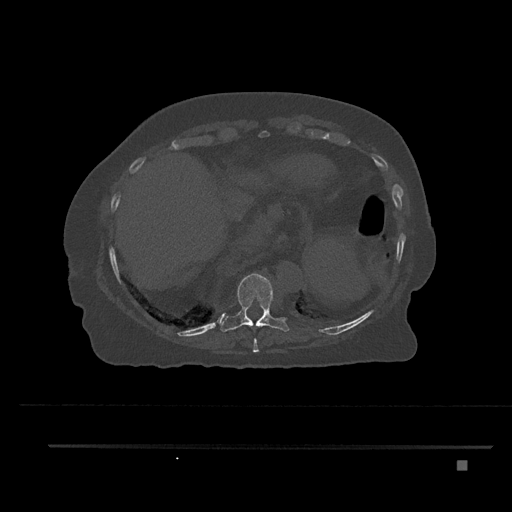
CT including the spine, one axial slice. Position 360 of 797 along the scan axis. Reconstruction kernel Br40s/3. 120 kVp. Bone window (W 1800 / L 400 HU). 0.5 mm slice thickness. 512 × 512 image matrix. Female patient, age 76 years. From the clinical record (not read from this slice): primary cancer: lung.
Structures marked on this image (semi-automatic segmentation, software-assisted and operator-edited):
- T10 vertebra: bounding box <220,273,289,332> (left, top, right, bottom; pixels)
- T9 vertebra: <253,337,259,353>